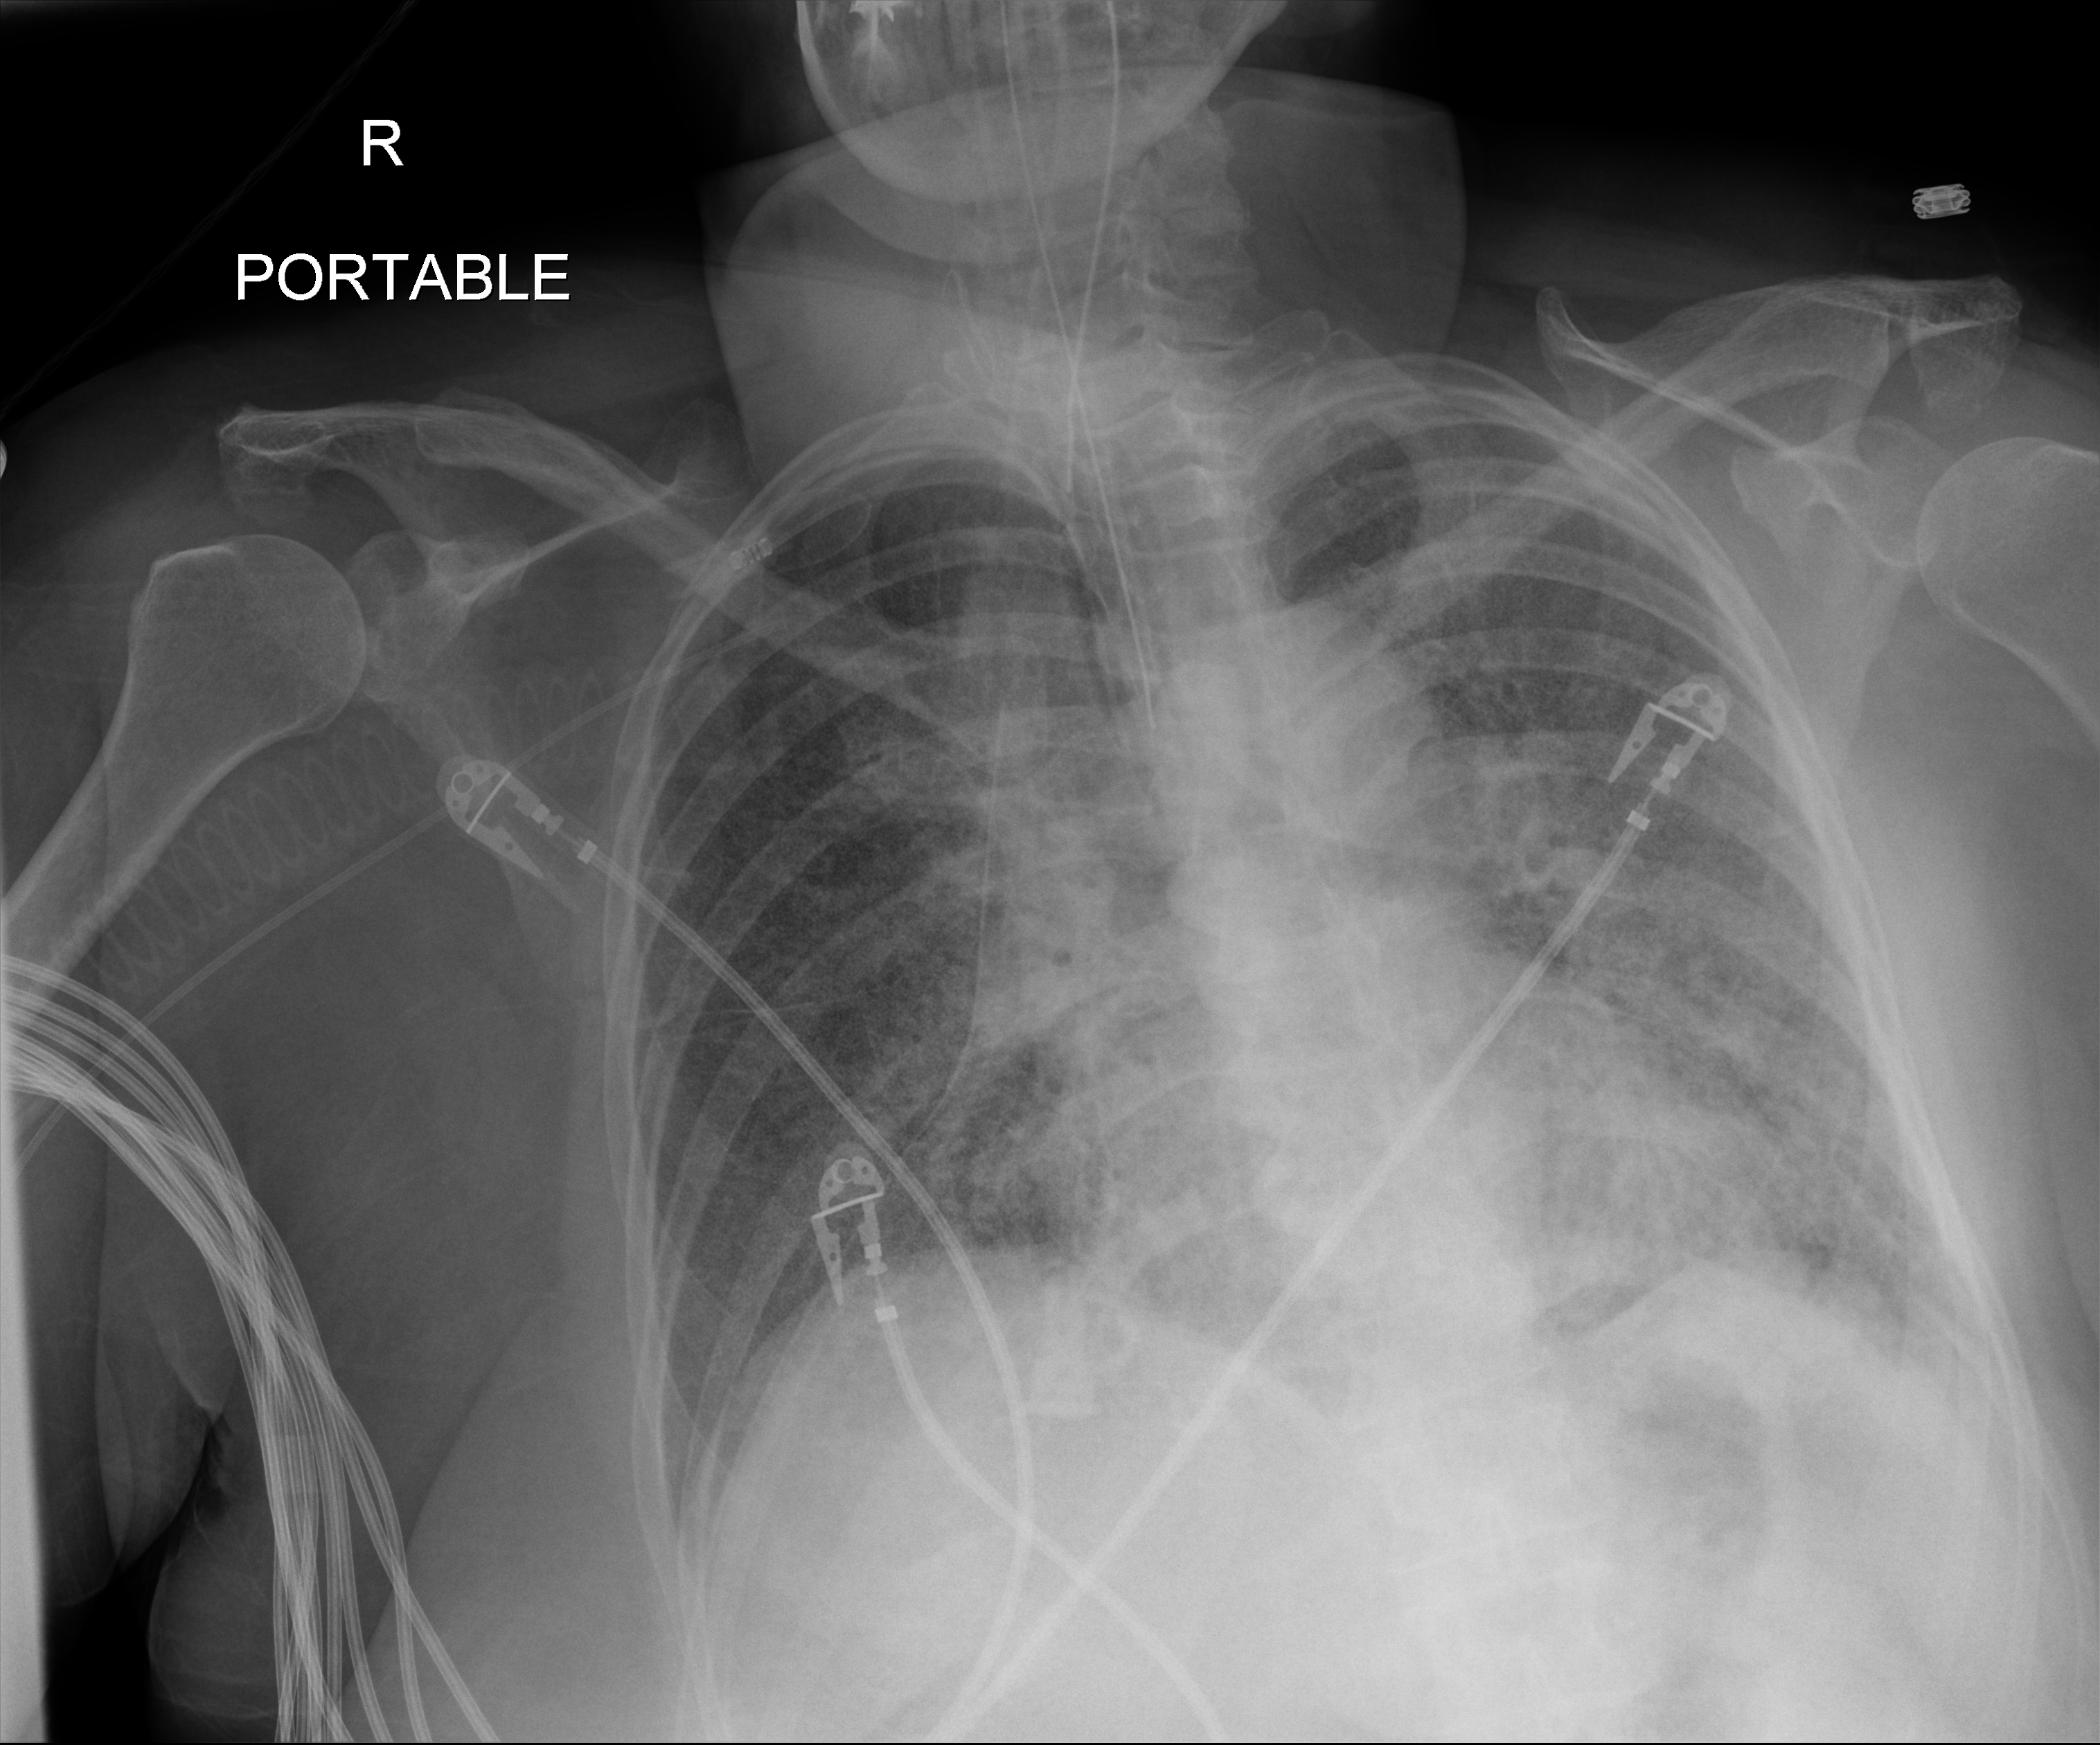
Bedside chest radiograph (digital radiography), anteroposterior (AP) projection. Patient hospitalised with COVID-19; female, aged 60–74 years.
Hospital-stay facts (about this admission, not read from this image; timing relative to this image not recorded): admitted to intensive care during this hospital stay: yes; length of hospital stay: 38 days; mechanically ventilated during this hospital stay: yes.